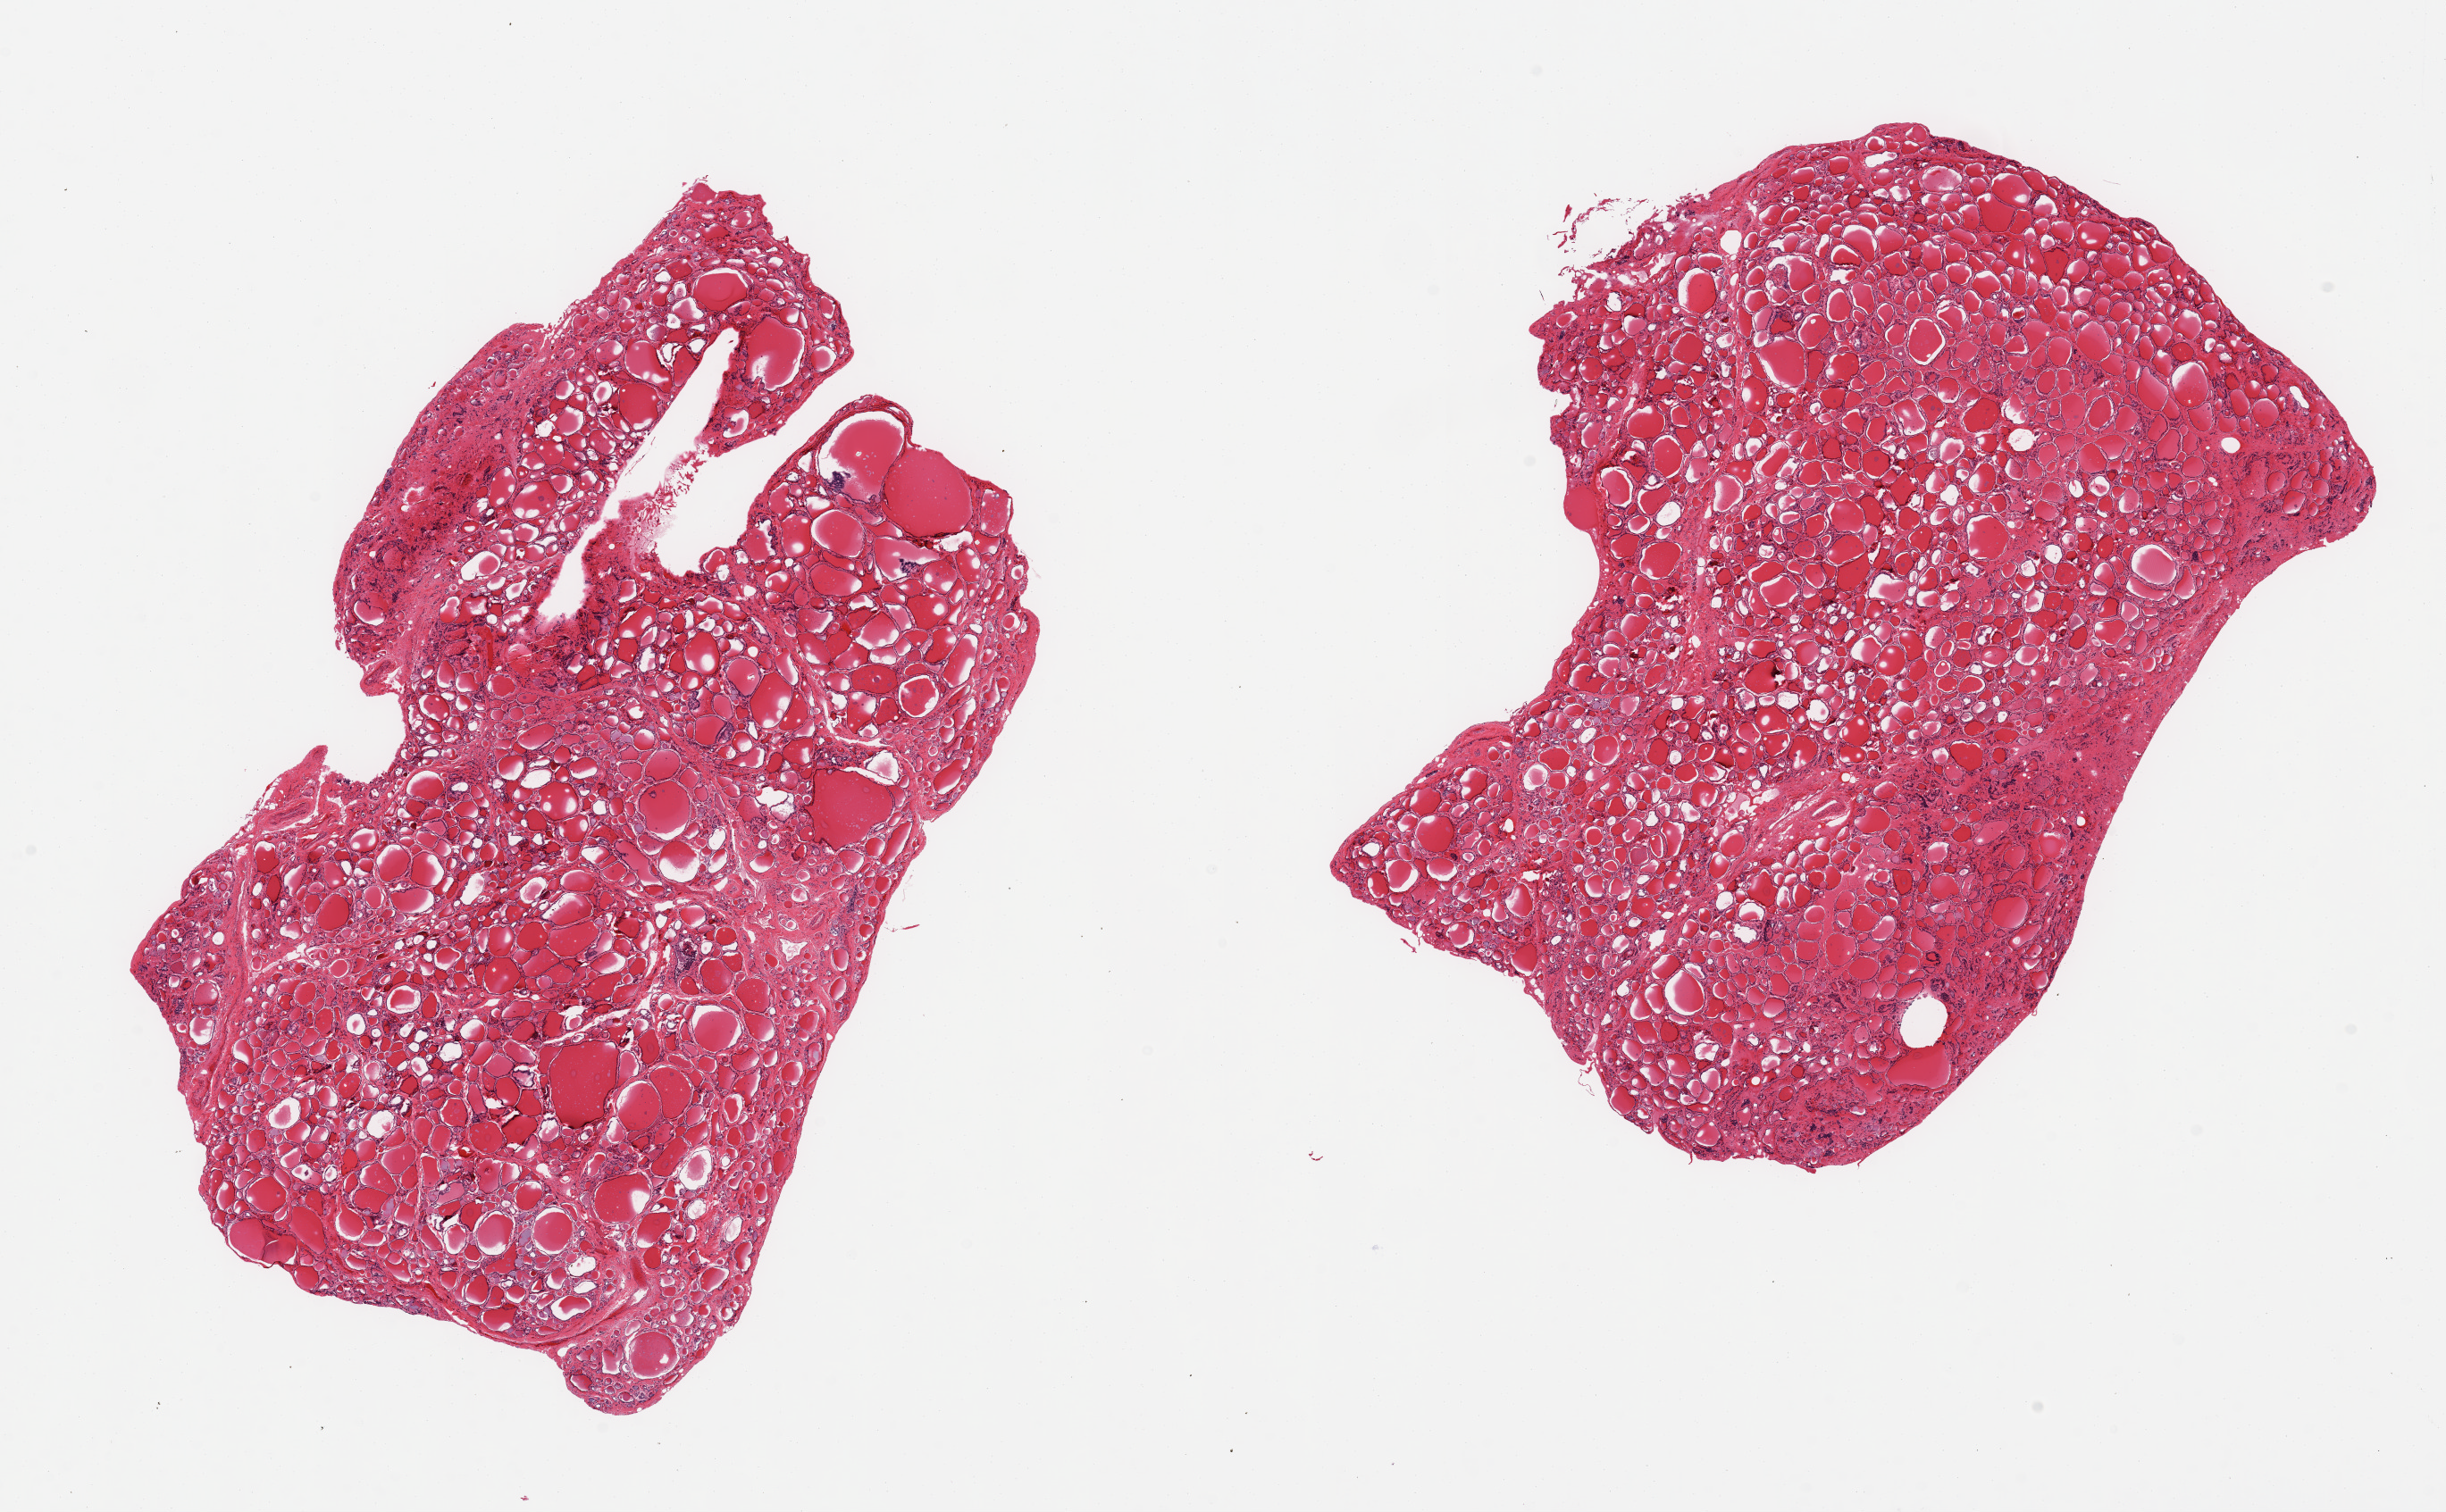
Digitized hematoxylin and eosin (H&E)-stained section, low-resolution overview of the scanned area, about 21.7 x 13.4 mm (slide scanned at 20x), PAXgene-fixed, paraffin-embedded tissue, sampled site (target tissue): thyroid, tissue donor sample. Male donor.
Review note (as recorded): 2 pieces; no lesions.